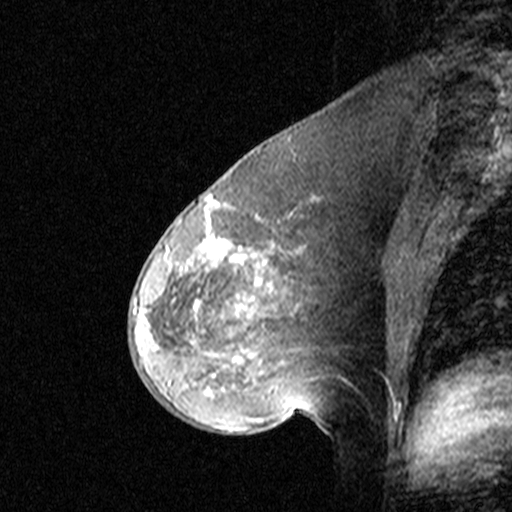
Breast MRI (dynamic contrast-enhanced), one sagittal slice; position 21 of 44 along the scan axis; dynamic contrast-enhanced study with each time point stored as its own series, time point 2 of 3 at this slice position (early post-contrast, ordered by acquisition time); 1.5 T; TE 4.5 ms, TR 11 ms; 3 mm slice thickness; 512 × 512 image matrix. Female patient, age 46 years. Case-level facts recorded for this patient, not image findings: setting: breast cancer imaged before/during neoadjuvant chemotherapy; receptor status: HER2-positive.
Annotated regions visible in this slice (semi-automatically segmented with operator editing):
- analysis volume of interest (the breast-tissue region the enhancement analysis was run in; not a lesion): bounding box [x1, y1, x2, y2] px = [144, 172, 359, 393]
- tumour enhancement mask (voxels above the 90 % enhancement threshold inside the analysis volume of interest): [144, 195, 315, 390]